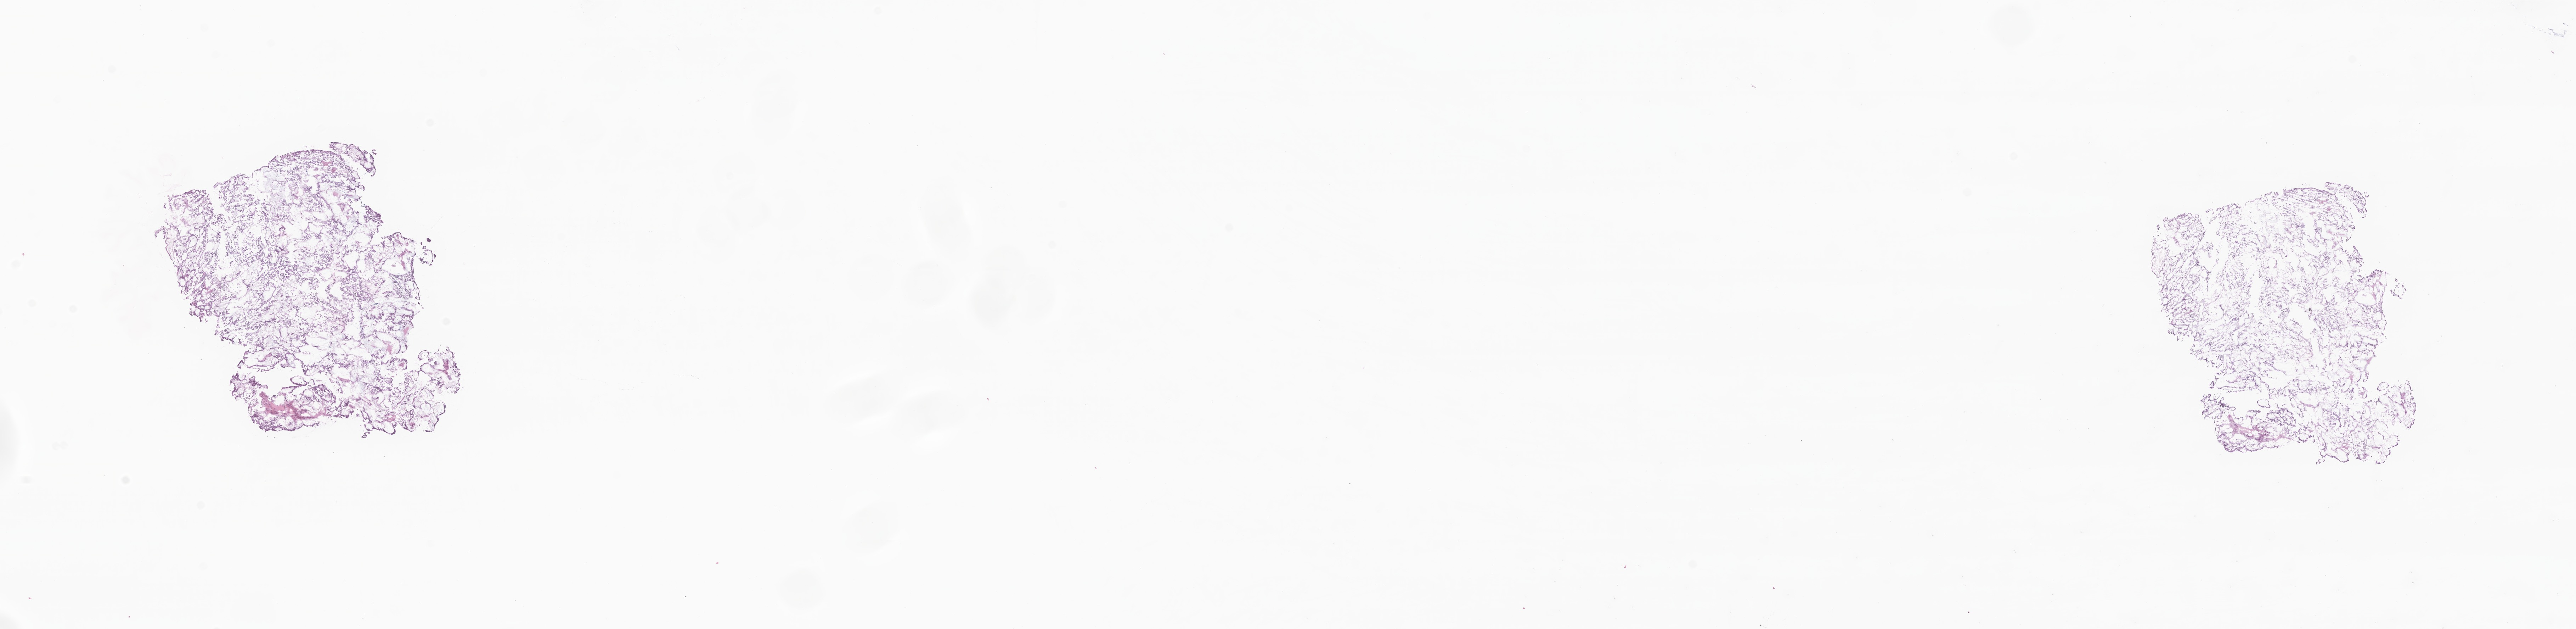
Digitized H&E-stained section of tumor tissue from the spinal cord — low-resolution overview of the scanned area, about 30.7 x 7.5 mm, frozen section. Male patient, age 193 months (16 years 1 month).
• recorded diagnosis: Myxopapillary ependymoma